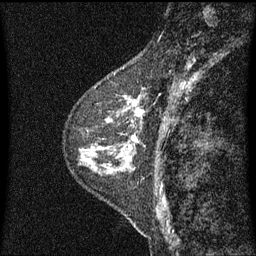
Breast MRI (dynamic contrast-enhanced), one sagittal slice; slice 20 of 60 in the series (ordered by position); dynamic contrast-enhanced series, image 2 of 3 at this slice position (ordered by acquisition); 1.5 T; TE 4.2 ms, TR 8 ms; 2 mm slice thickness; 256 × 256 image matrix, field of view 200 × 200 mm. Patient: female, 48 years.
Annotated regions visible in this slice (semi-automatic segmentation, software-assisted and operator-edited):
- analysis volume of interest (the breast-tissue region the enhancement analysis was run in; not a lesion): bounding box <103,74,145,139> (left, top, right, bottom; pixels)
- tumour enhancement mask (voxels above the 70 % enhancement threshold inside the analysis volume of interest): <111,88,145,139>